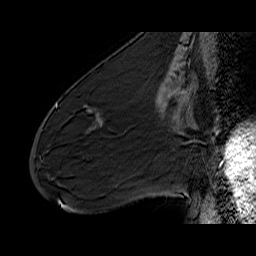
Breast MRI (dynamic contrast-enhanced), one sagittal slice; position 26 of 60 along the scan axis; dynamic contrast-enhanced series, time point 2 of 6 at this slice position (early post-contrast); 1.5 T; TE 6.5 ms, TR 32.9 ms; 256 × 256 image matrix, field of view 200 × 200 mm. Female patient. From the clinical record (not read from this slice): setting: breast cancer imaged before/during neoadjuvant chemotherapy; receptor status: HER2-positive.
Annotated regions visible in this slice (semi-automatically segmented with operator editing):
- analysis volume of interest (the breast-tissue region the enhancement analysis was run in; not a lesion): box from (x=72, y=88) to (x=133, y=137) px
- tumour enhancement mask (voxels above the 100 % enhancement threshold inside the analysis volume of interest): (x=88, y=121)–(x=102, y=131)